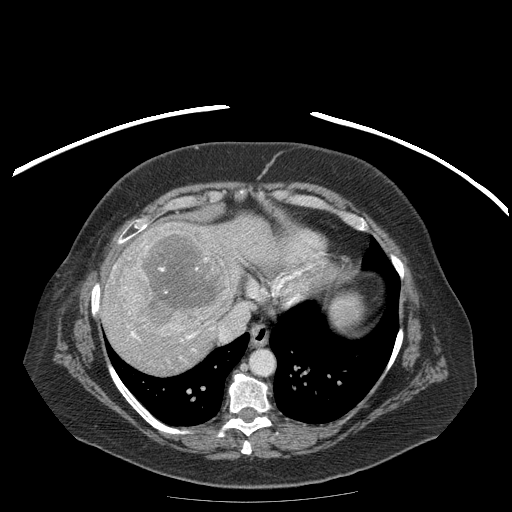
Contrast-enhanced abdominal CT (liver protocol), one axial slice; reconstruction kernel STANDARD; 120 kVp; soft-tissue window (W 400 / L 40 HU); 512 × 512 image matrix, field of view 440 × 440 mm. From the clinical record (not read from this slice): diagnosis: hepatocellular carcinoma (patient treated with transarterial chemoembolisation; whether this scan precedes or follows treatment is not stated here); TNM stage (as recorded): Stage-IIIB; Child-Pugh class: A; tumour differentiation: well differentiated; tumour nodularity: uninodular.
Annotated regions visible in this slice (semi-automatic segmentation, software-assisted and operator-edited):
- liver parenchyma outside the tumour (the mass and vessels are separate outlines, so this box may not span the whole liver): bounding box (x1, y1, x2, y2) in pixels: (100, 216, 284, 374)
- mass: (121, 231, 229, 336)
- liver vessels: (114, 266, 213, 351)